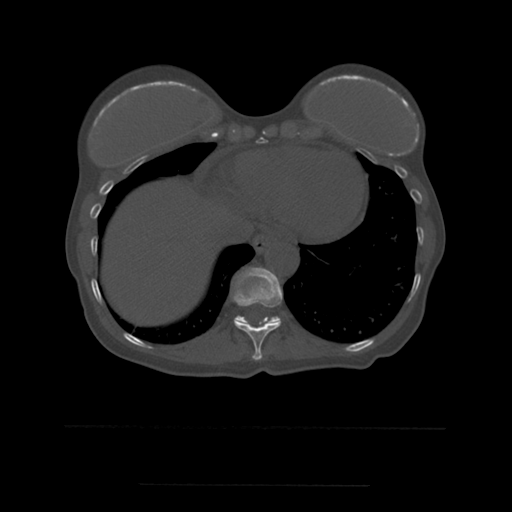
CT including the spine, one axial slice; slice 295 of 544 in the series (ordered by position); bone window (W 1800 / L 400 HU); 512 × 512 image matrix, field of view 350 × 350 mm. Patient age 58 years. Case-level facts recorded for this patient, not image findings: primary cancer: lung.
Structures marked on this image (semi-automatic segmentation, software-assisted and operator-edited):
- T10 vertebra: bounding box [x1, y1, x2, y2] px = [233, 268, 283, 361]
- T11 vertebra: [234, 316, 281, 324]